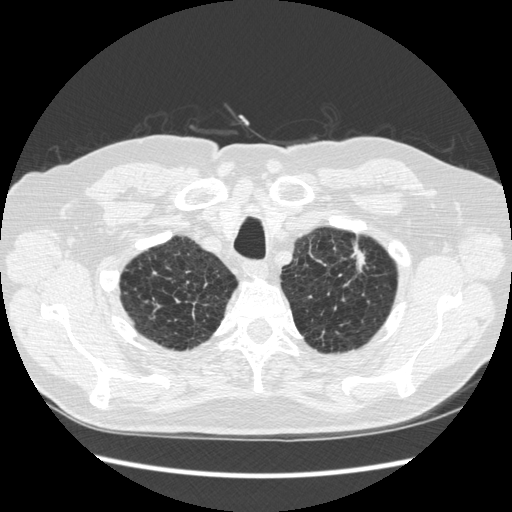
Axial slice from a low-dose chest CT screening exam. Third screening round (two years after baseline). Lung window (W 1500 / L -600 HU). 1.25 mm slice thickness. Slice 31 of 267 in the series. 512 × 512 image matrix, field of view 360 × 360 mm. Male, age 70 years at enrolment.
Lesion marked by an expert reader, bounding box <324,233,379,298> (left, top, right, bottom; pixels). The screening reader recorded 2 non-calcified nodules or masses ≥4 mm on this exam; which of them this box marks is not recorded. Official screen result: positive, other. Later outcome: lung cancer diagnosed 92 days after this screen — squamous cell carcinoma, NOS, left upper lobe, moderately differentiated (G2), stage IA (AJCC 6th edition), 18 mm at pathology.